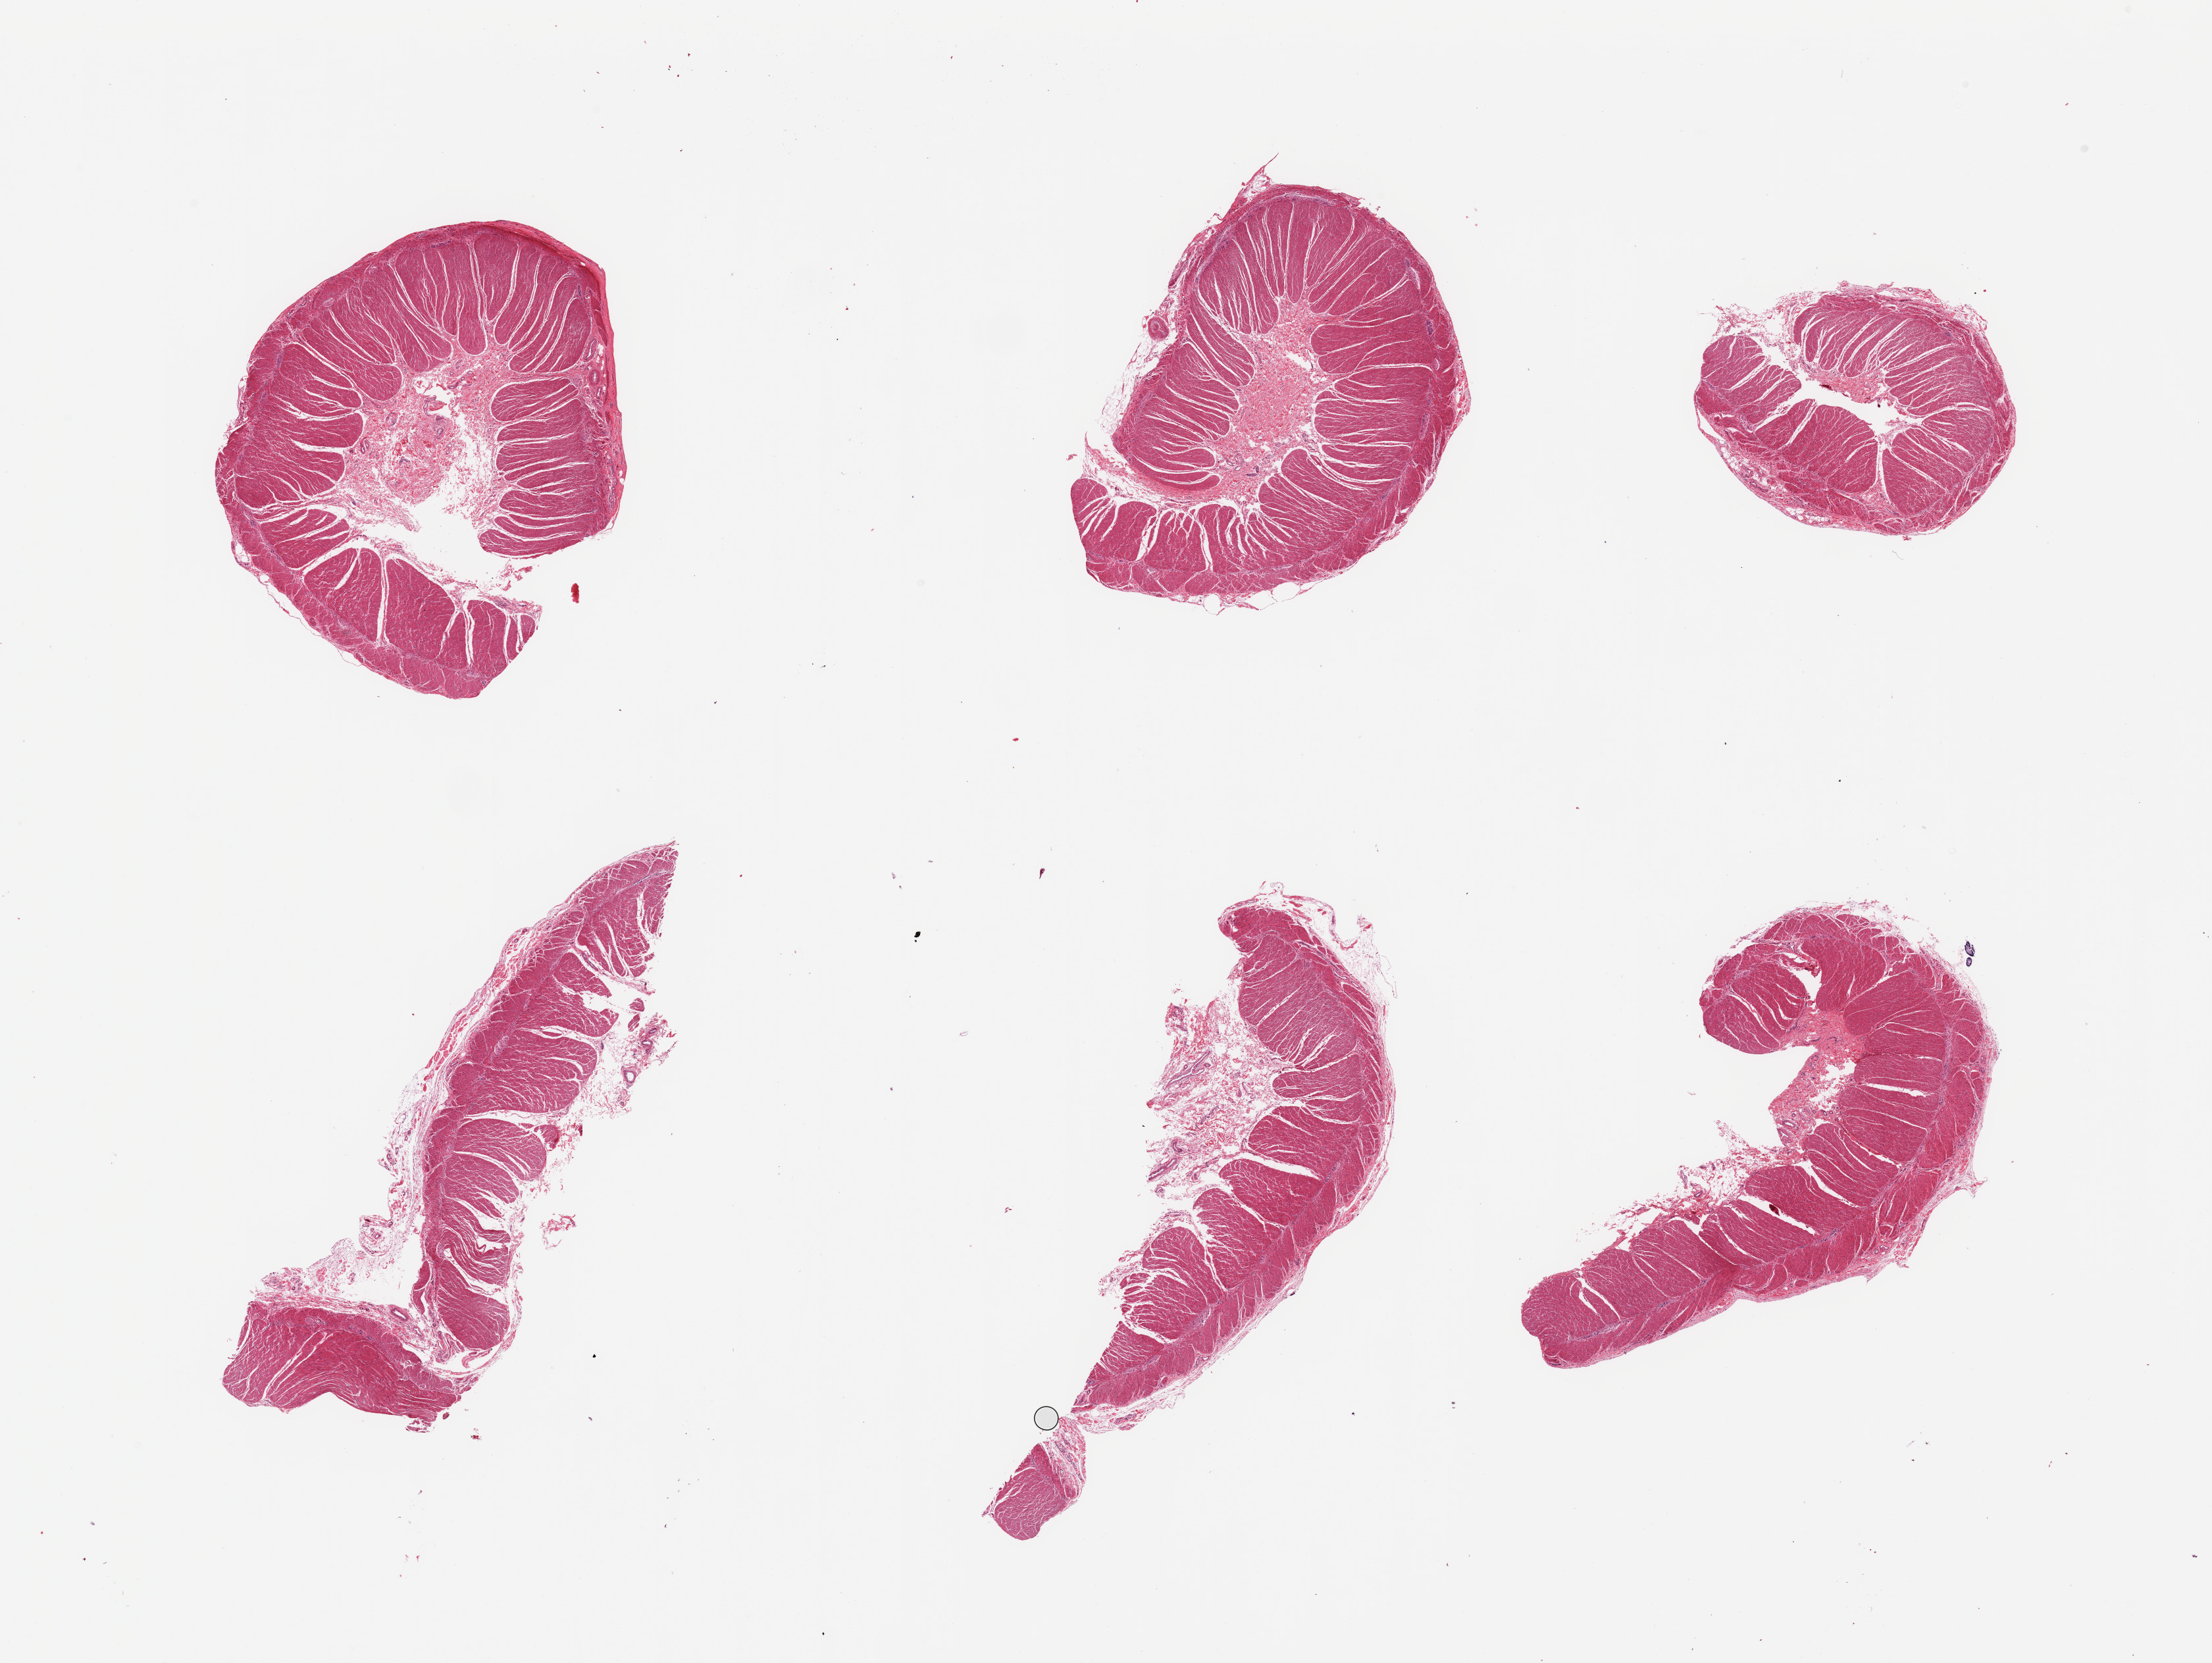
H&E whole-slide image — a low-resolution overview of the entire scanned area, about 26.6 x 20.0 mm. PAXgene-fixed, paraffin-embedded tissue. Section of sigmoid colon (target tissue). Donor tissue sample. Female donor.
Review note (as recorded): 6 pieces; well dissected muscularis propria.